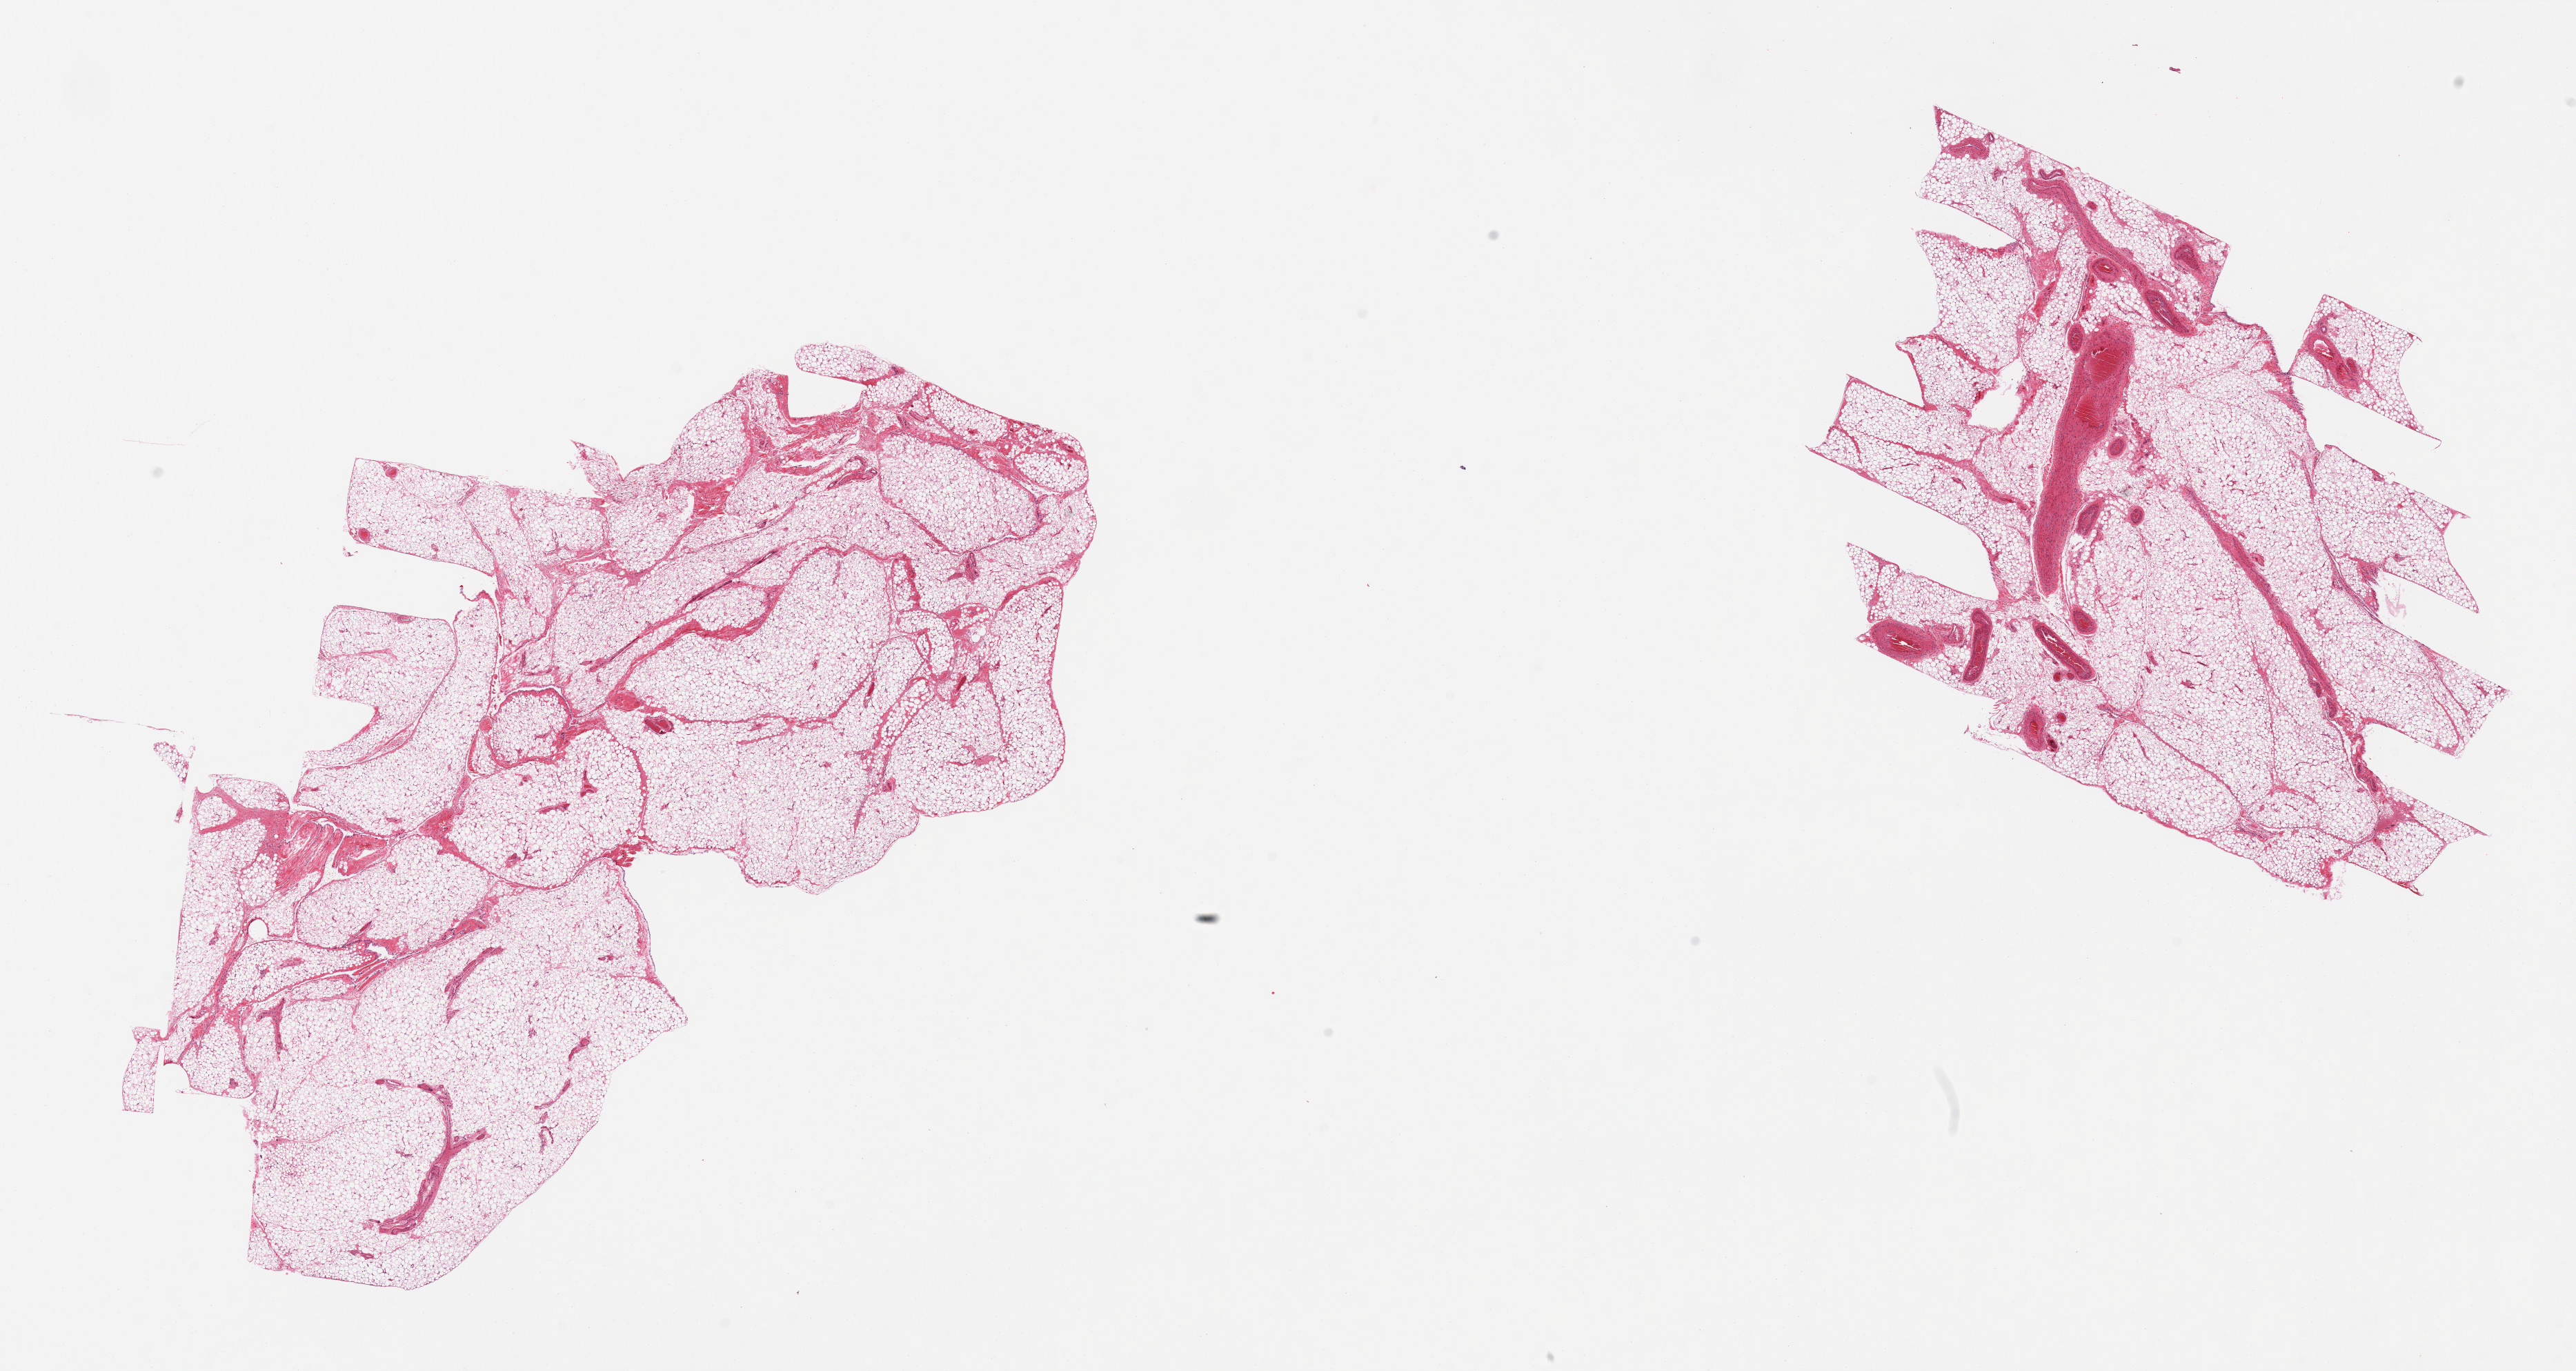
Digitized hematoxylin and eosin (H&E)-stained section, whole scanned area (about 29.5 x 15.7 mm) shown as a low-resolution overview, PAXgene-fixed paraffin-embedded (PFPE) section, section of omentum (target tissue), tissue donor sample.
Review note (as recorded): 2 pieces; ~10% fibrosvascular tissue, moderate mesothelial prominence/hyperplasia.